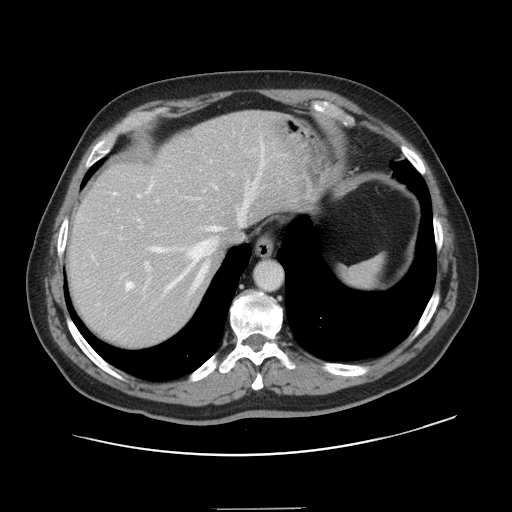
Contrast-enhanced abdominal CT, one axial slice. Slice 117 of 143 in the series (ordered by position). 120 kVp. Intravenous contrast given. Soft-tissue window (W 400 / L 40 HU). 2.5 mm slice thickness. 512 × 512 image matrix. Male patient, age 62 years. Case-level facts recorded for this patient, not image findings: diagnosis: colorectal cancer liver metastases, imaged before liver resection; multiple liver metastases: yes; largest metastasis: 2.7 cm.
Annotated regions visible in this slice (expert manual segmentation):
- hepatic veins: box from (x=114, y=148) to (x=264, y=291) px
- liver: (x=69, y=113)–(x=304, y=347)
- planned liver remnant (the part of the liver to remain after resection): (x=69, y=113)–(x=303, y=287)
- portal vein (with intrahepatic branches): (x=120, y=144)–(x=265, y=283)